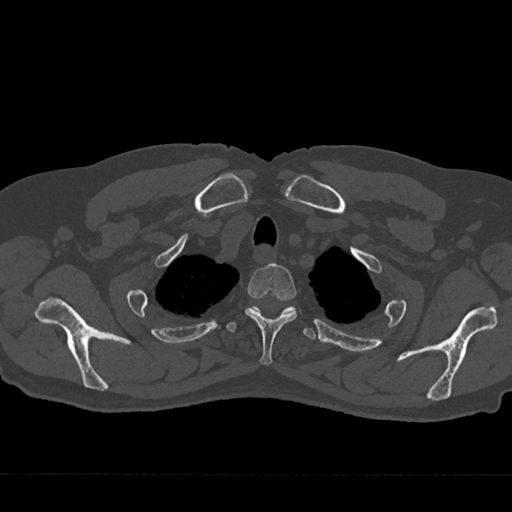
CT including the spine, one axial slice; slice 602 of 797 in the series (ordered by position); reconstruction kernel Br40s/3; 120 kVp; bone window (W 1800 / L 400 HU); 512 × 512 image matrix. Patient: male, 75 years. Case-level facts recorded for this patient, not image findings: primary cancer: renal.
Annotated regions visible in this slice (semi-automatic segmentation, software-assisted and operator-edited):
- T2 vertebra: box from (x=245, y=263) to (x=297, y=365) px
- T3 vertebra: (x=227, y=306)–(x=316, y=340)